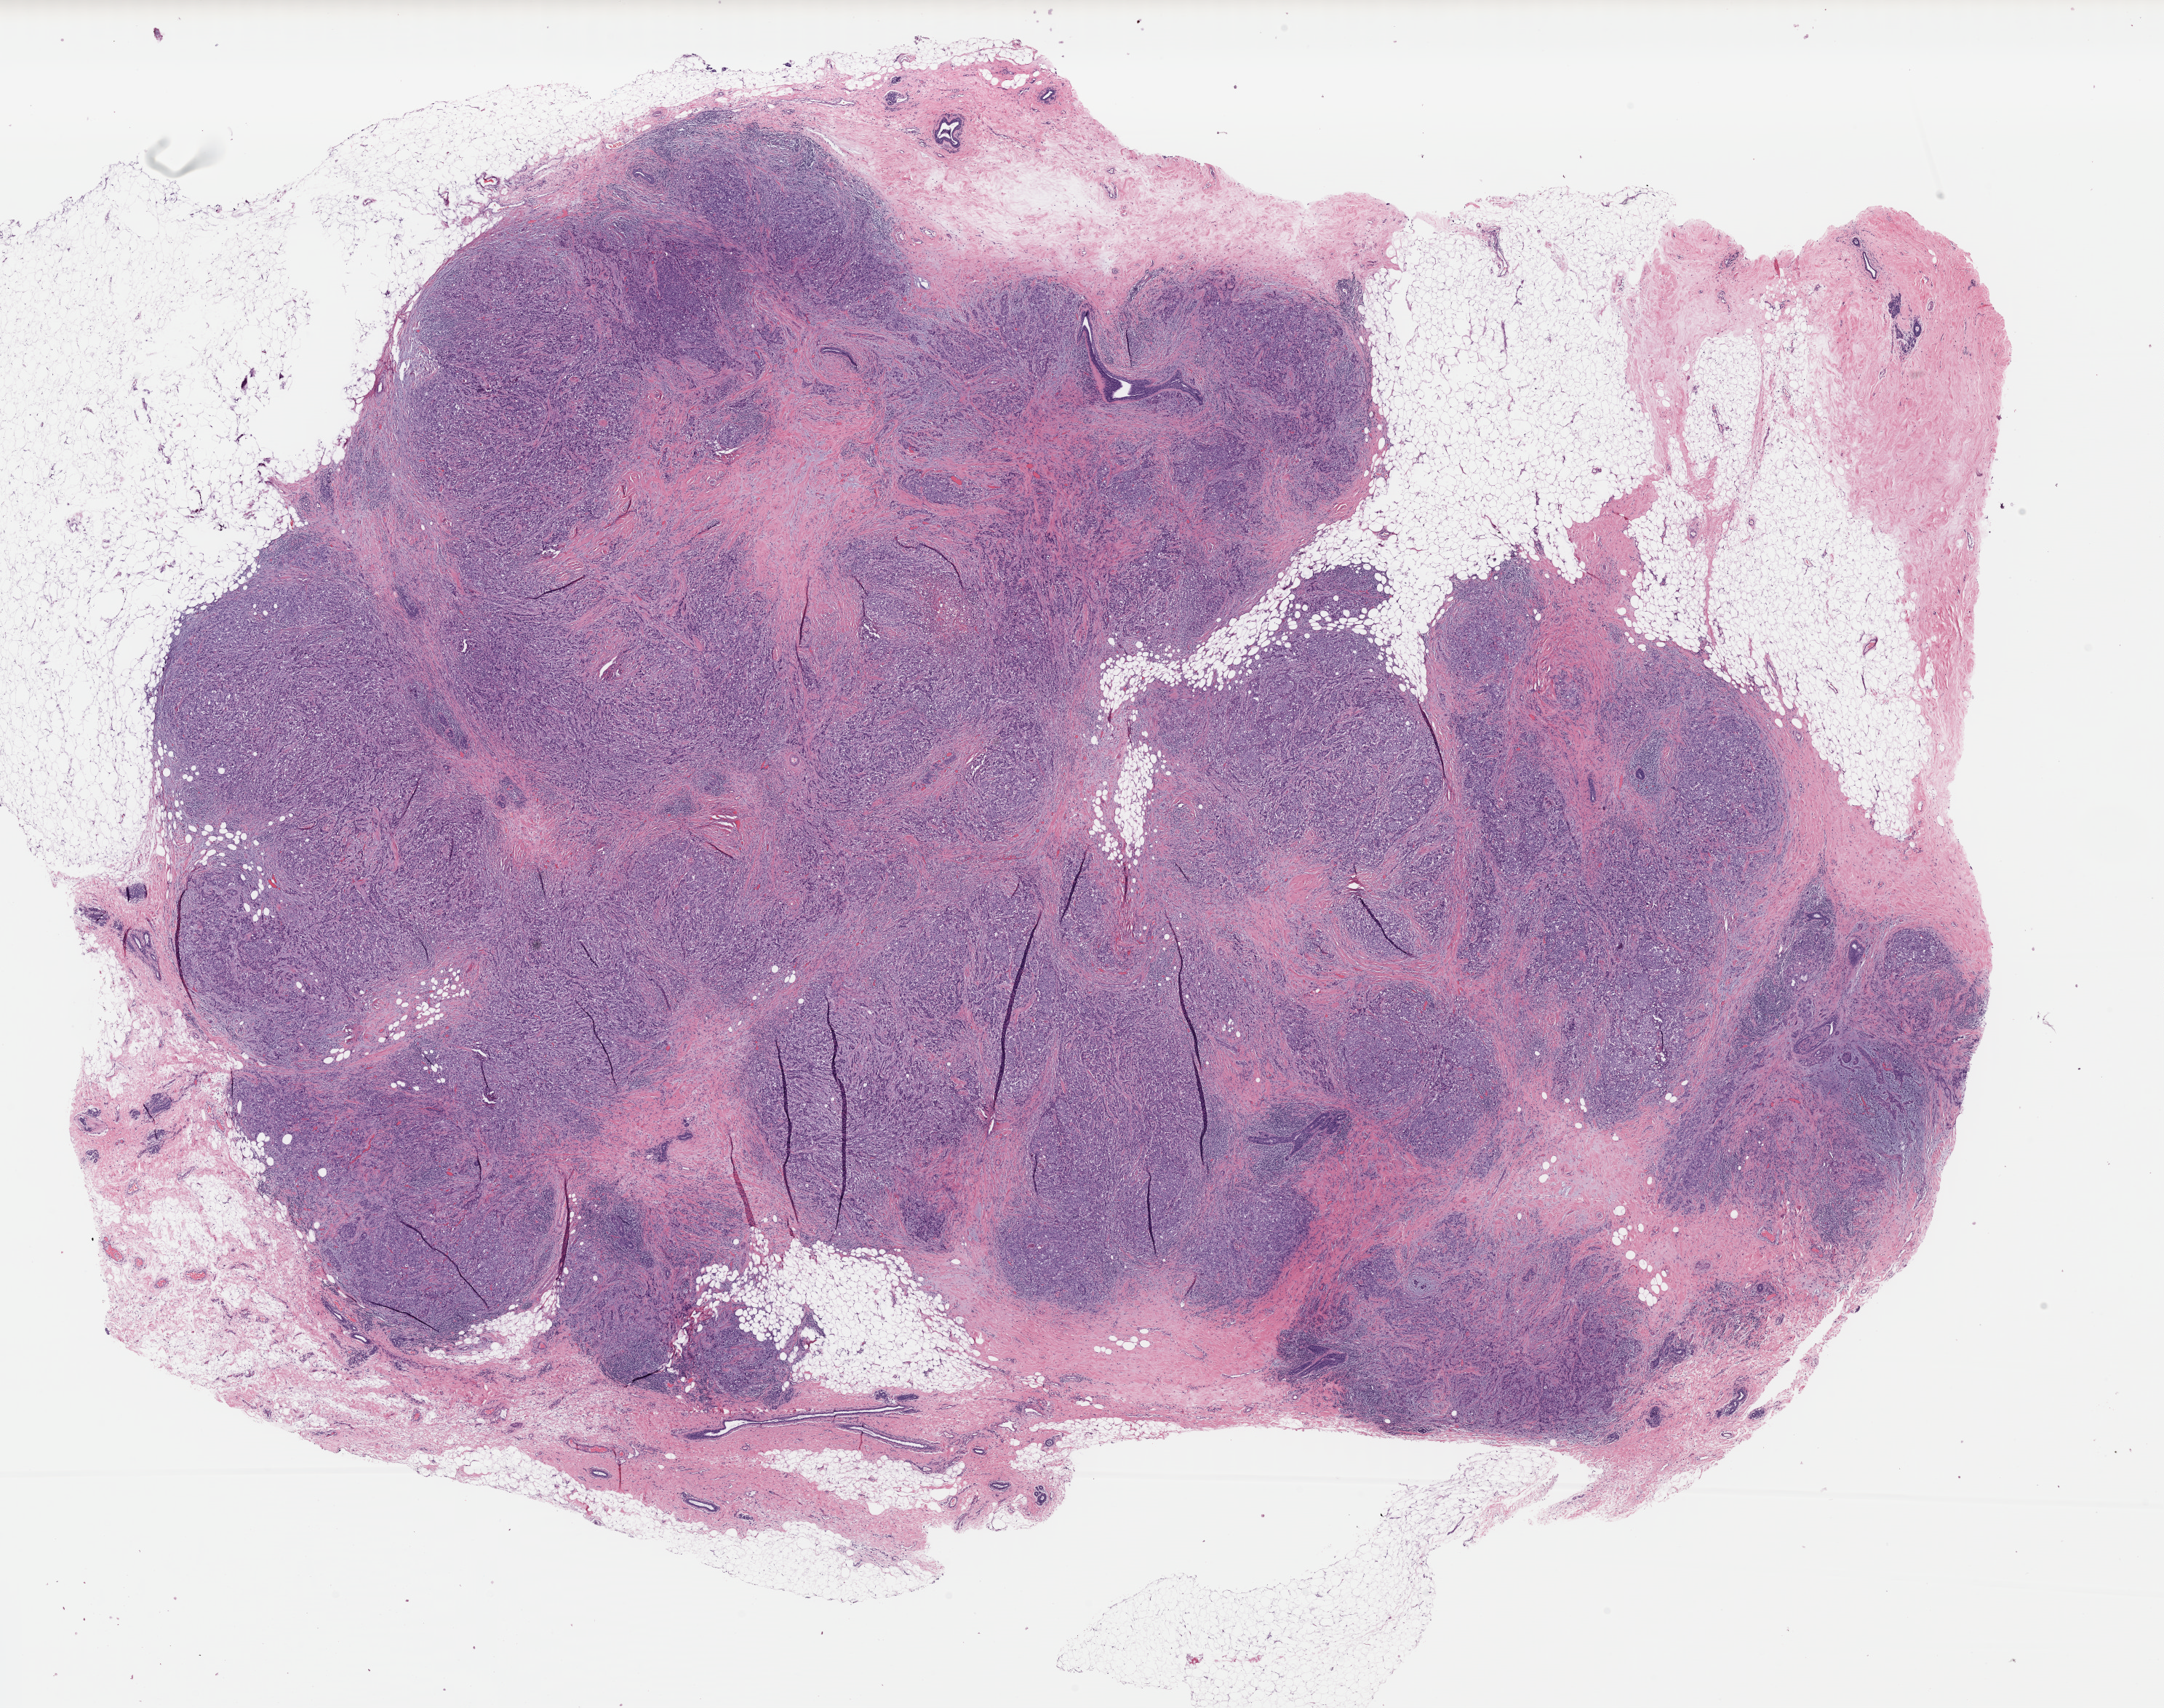
Digitized H&E tissue section (whole slide) — shown as a low-resolution overview of the whole scanned area (about 23.5 x 18.5 mm, slide scanned at 40x); FFPE section; primary tumour sample from the breast. Patient: female, age at initial diagnosis 59 years.
Pathologic diagnosis: Infiltrating duct carcinoma, NOS.